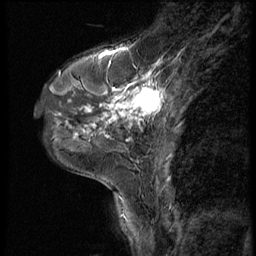
Breast MRI (dynamic contrast-enhanced), one sagittal slice; slice 20 of 56 in the series (ordered by position); 3 images stored at this slice position (order not interpretable as contrast timing); 1.5 T; TE 4.2 ms, TR 9 ms; 2.5 mm slice thickness; 256 × 256 image matrix, field of view 180 × 180 mm. Female patient, age 46 years. Case-level facts recorded for this patient, not image findings: setting: breast cancer imaged before/during neoadjuvant chemotherapy; receptor status: HER2-positive.
Structures marked on this image (semi-automatic segmentation, software-assisted and operator-edited):
- analysis volume of interest (the breast-tissue region the enhancement analysis was run in; not a lesion): bounding box (x1, y1, x2, y2) in pixels: (79, 68, 190, 143)
- tumour enhancement mask (voxels above the 140 % enhancement threshold inside the analysis volume of interest): (85, 72, 164, 134)